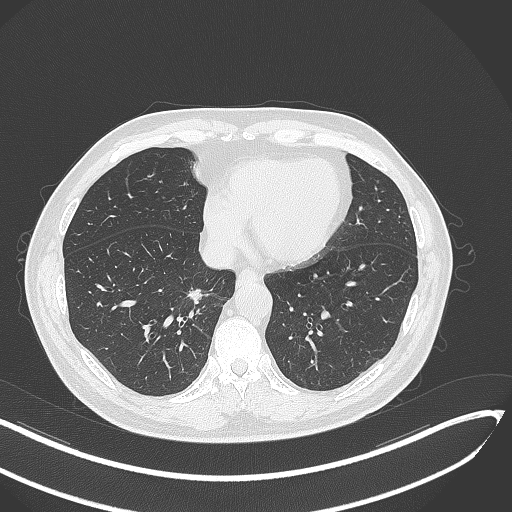
Chest CT, one axial slice. Position 122 of 429 along the scan axis. Reconstruction kernel B70f. 120 kVp. Lung window (W 1500 / L -600 HU). 512 × 512 image matrix, field of view 400 × 400 mm. Male patient, age 62 years. From the clinical record (not read from this slice): clinical TNM (as recorded): T1b N0 M0; histopathological grade: G2.
Structures marked on this image (rectangle marked by the reading radiologist):
- lung tumour (recorded histology: adenocarcinoma): bounding box <180,283,223,308> (left, top, right, bottom; pixels)